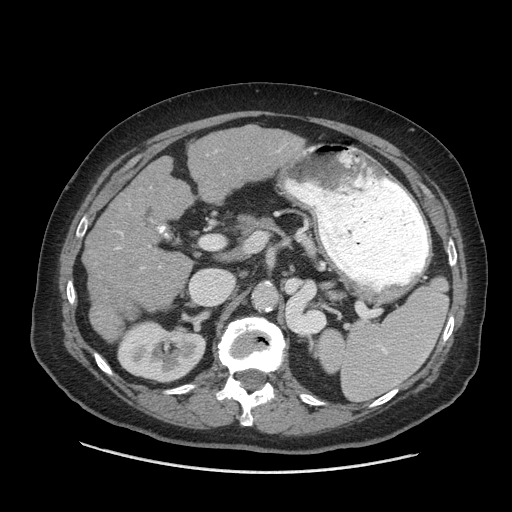
Contrast-enhanced abdominal CT (liver protocol), one axial slice; position 32 of 77 along the scan axis; reconstruction kernel STANDARD; 140 kVp; soft-tissue window (W 400 / L 40 HU); 2.5 mm slice thickness; 512 × 512 image matrix, field of view 420 × 420 mm. Case-level facts recorded for this patient, not image findings: diagnosis: hepatocellular carcinoma (patient treated with transarterial chemoembolisation; whether this scan precedes or follows treatment is not stated here); TNM stage (as recorded): Stage-I; Child-Pugh class: A; tumour nodularity: uninodular.
Annotated regions visible in this slice (semi-automatically segmented with operator editing):
- liver parenchyma outside the tumour (the mass and vessels are separate outlines, so this box may not span the whole liver): bounding box <84,126,310,321> (left, top, right, bottom; pixels)
- liver vessels: <115,150,279,249>